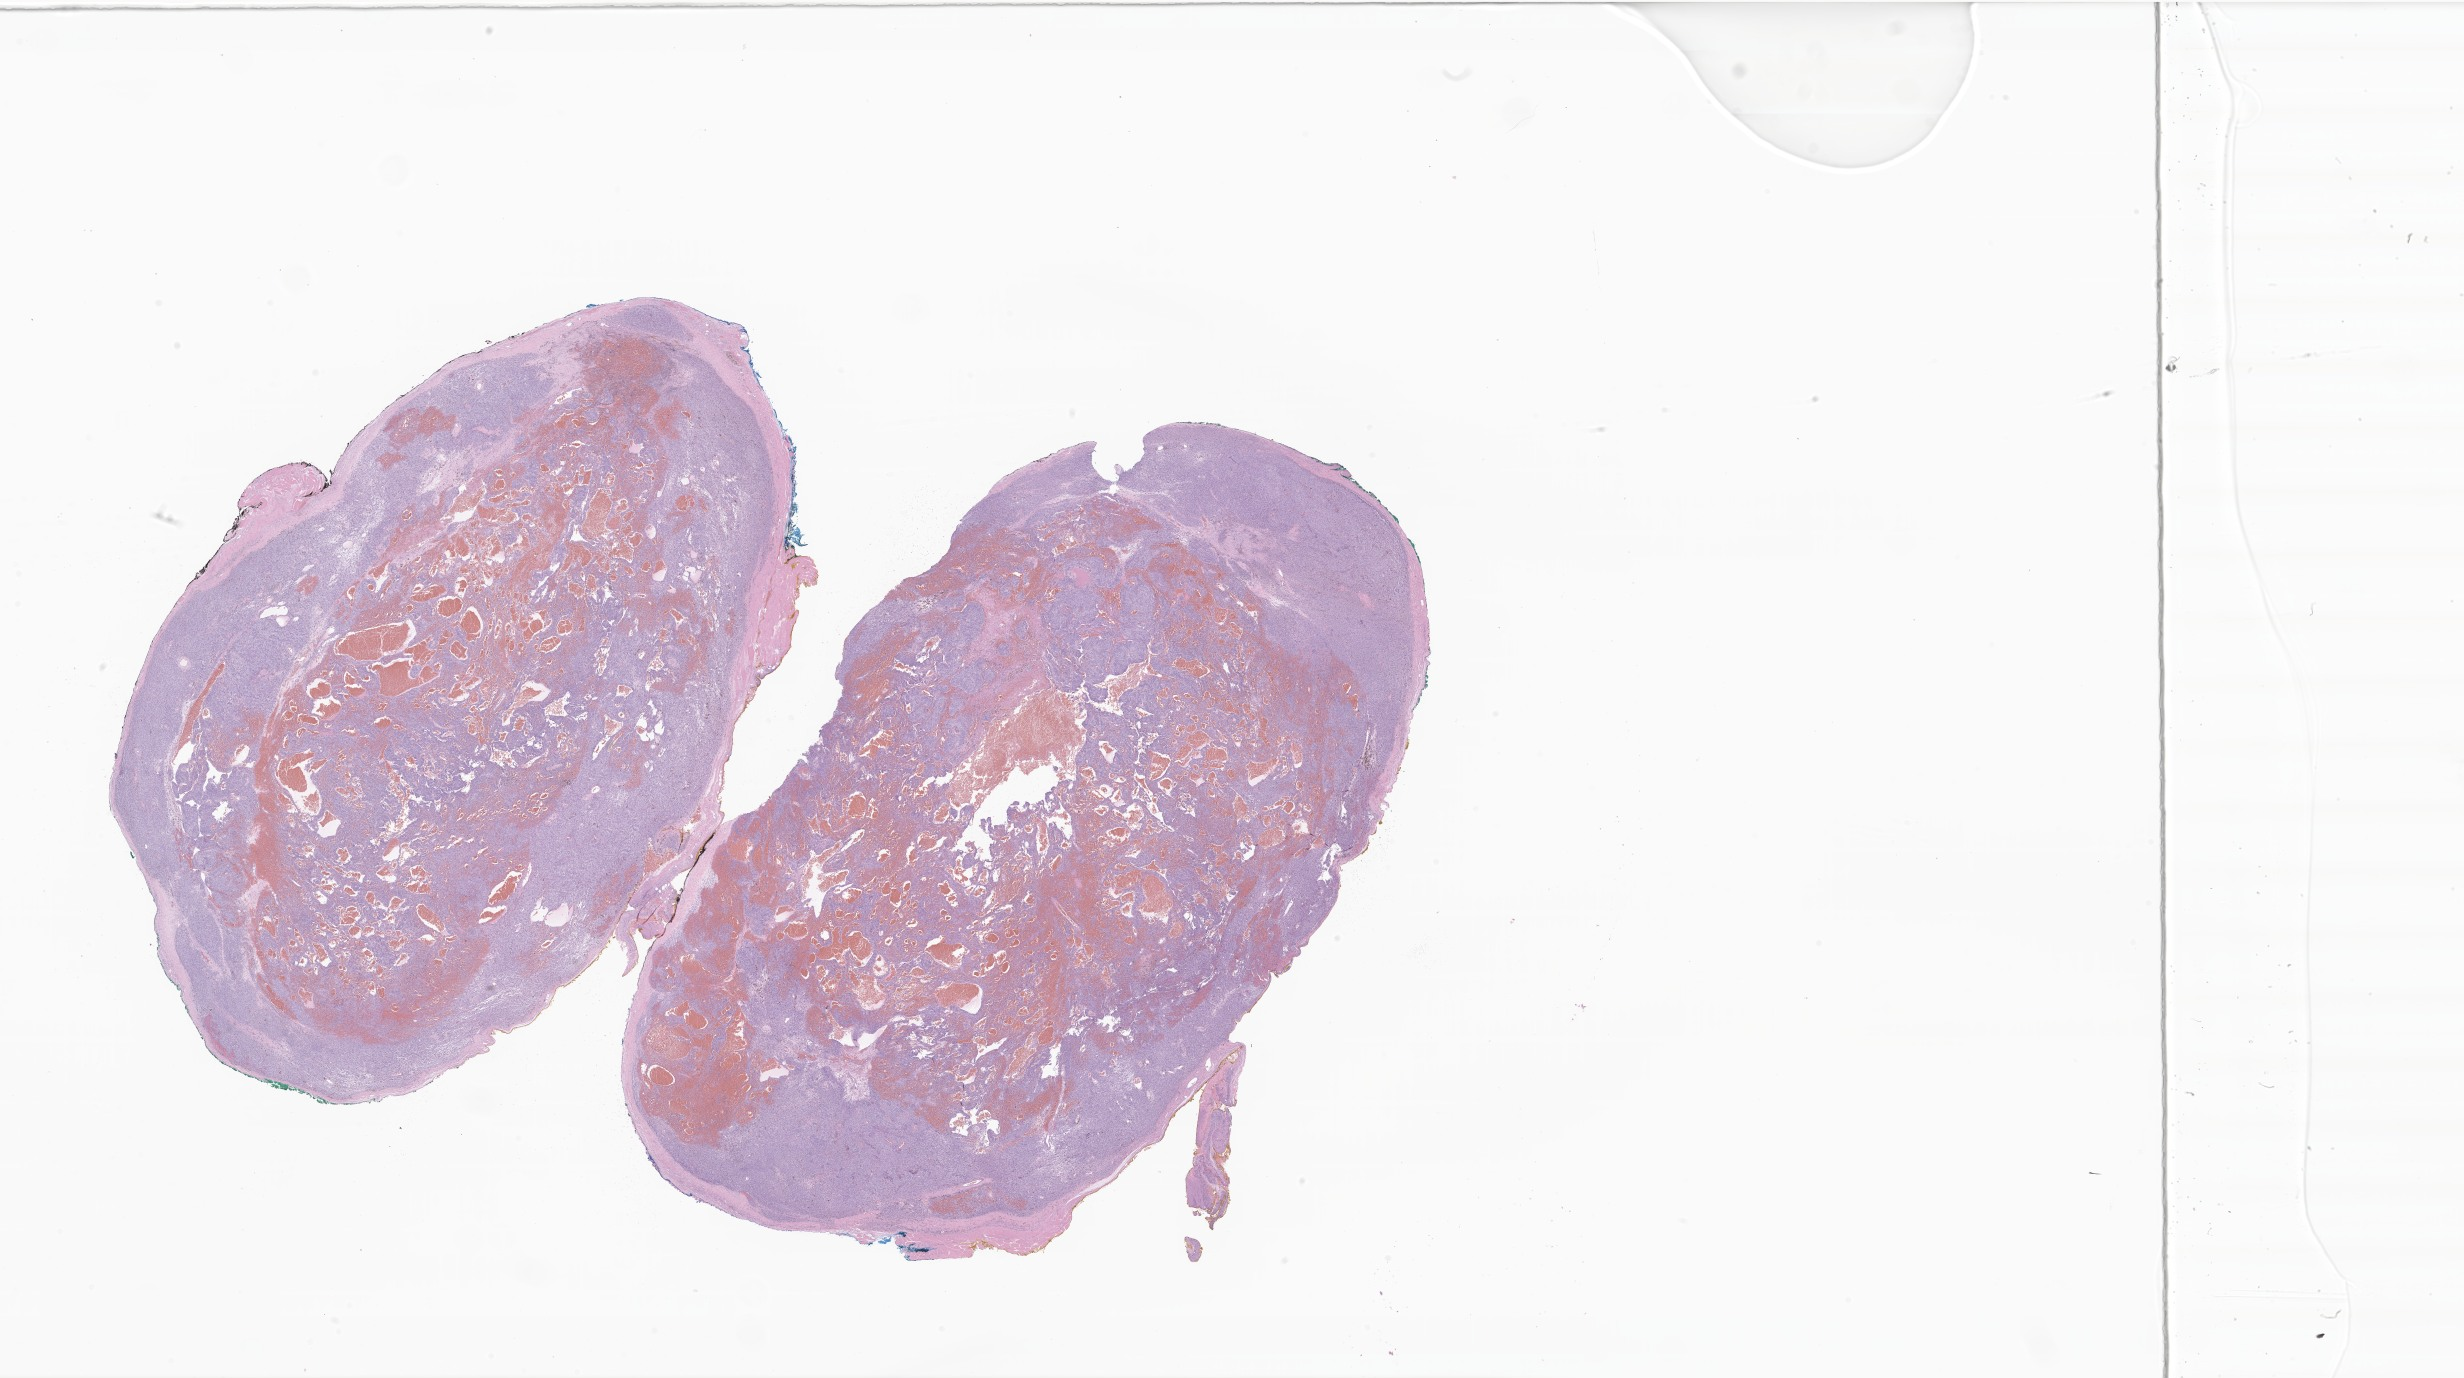
Digitized H&E-stained section of tumor tissue from the soft tissue, shown as a low-resolution overview of the whole scanned area (about 41.5 x 23.2 mm), FFPE section. Patient: male, age 140 months (11 years 8 months).
Recorded diagnosis: Neoplasm, malignant.